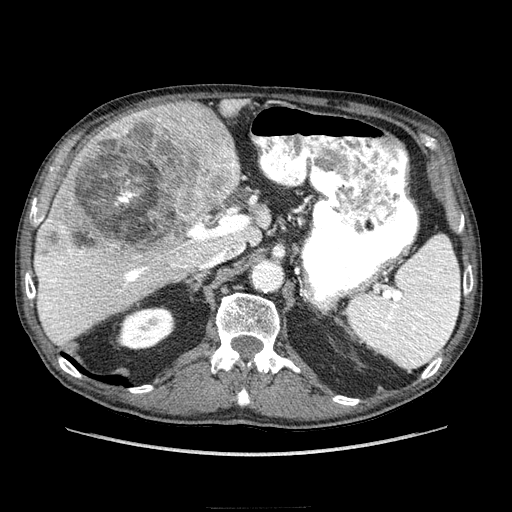
Contrast-enhanced abdominal CT (liver protocol), one axial slice. Position 149 of 218 along the scan axis. Reconstruction kernel STANDARD. Soft-tissue window (W 400 / L 40 HU). 512 × 512 image matrix, field of view 380 × 380 mm. Case-level facts recorded for this patient, not image findings: diagnosis: hepatocellular carcinoma (patient treated with transarterial chemoembolisation; whether this scan precedes or follows treatment is not stated here); TNM stage (as recorded): Stage-IIIA; Child-Pugh class: A.
Annotated regions visible in this slice (semi-automatic segmentation, software-assisted and operator-edited):
- liver parenchyma outside the tumour (the mass and vessels are separate outlines, so this box may not span the whole liver): box from (x=34, y=98) to (x=270, y=346) px
- mass: (x=37, y=100)–(x=239, y=270)
- liver vessels: (x=37, y=196)–(x=267, y=338)